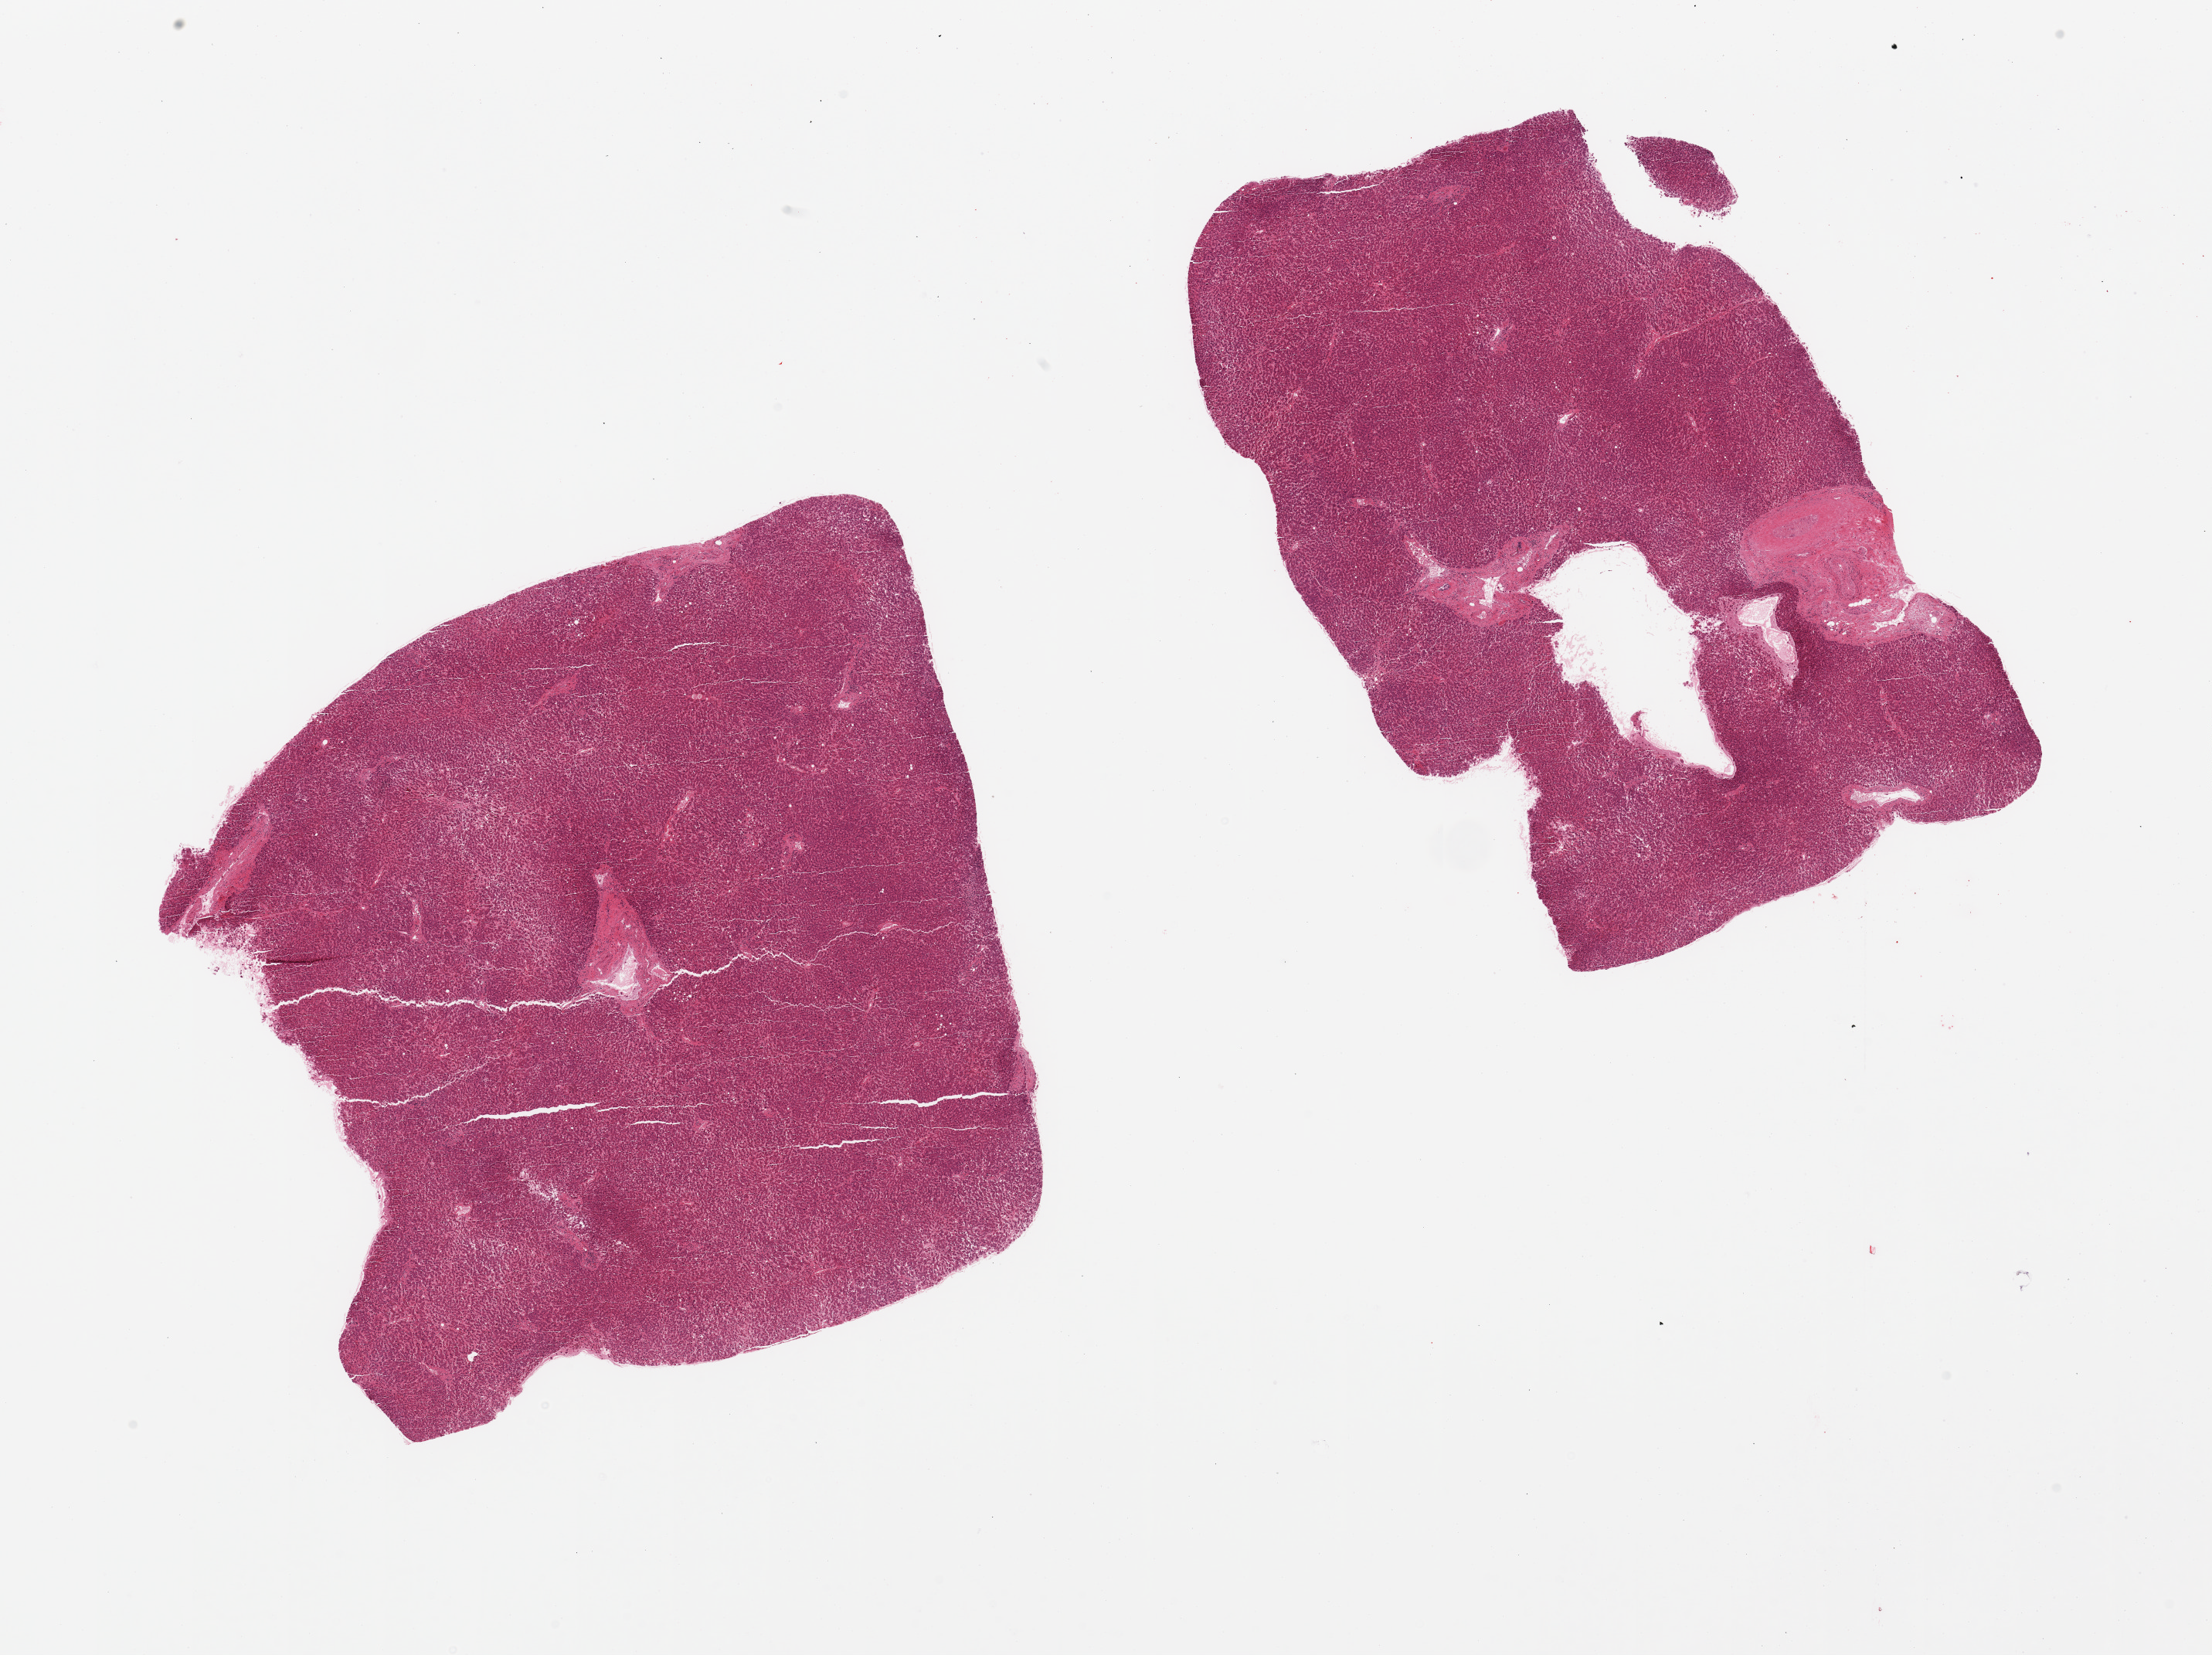
Haematoxylin and eosin whole-slide image — shown as a low-resolution overview of the whole scanned area (about 22.6 x 16.9 mm); PAXgene-fixed, paraffin-embedded tissue; section of liver (target tissue); tissue donor sample.
Reviewer comment on this tissue sample: 2 pieces; mild congestion, includes focus of larger vessels/duct/nerve.